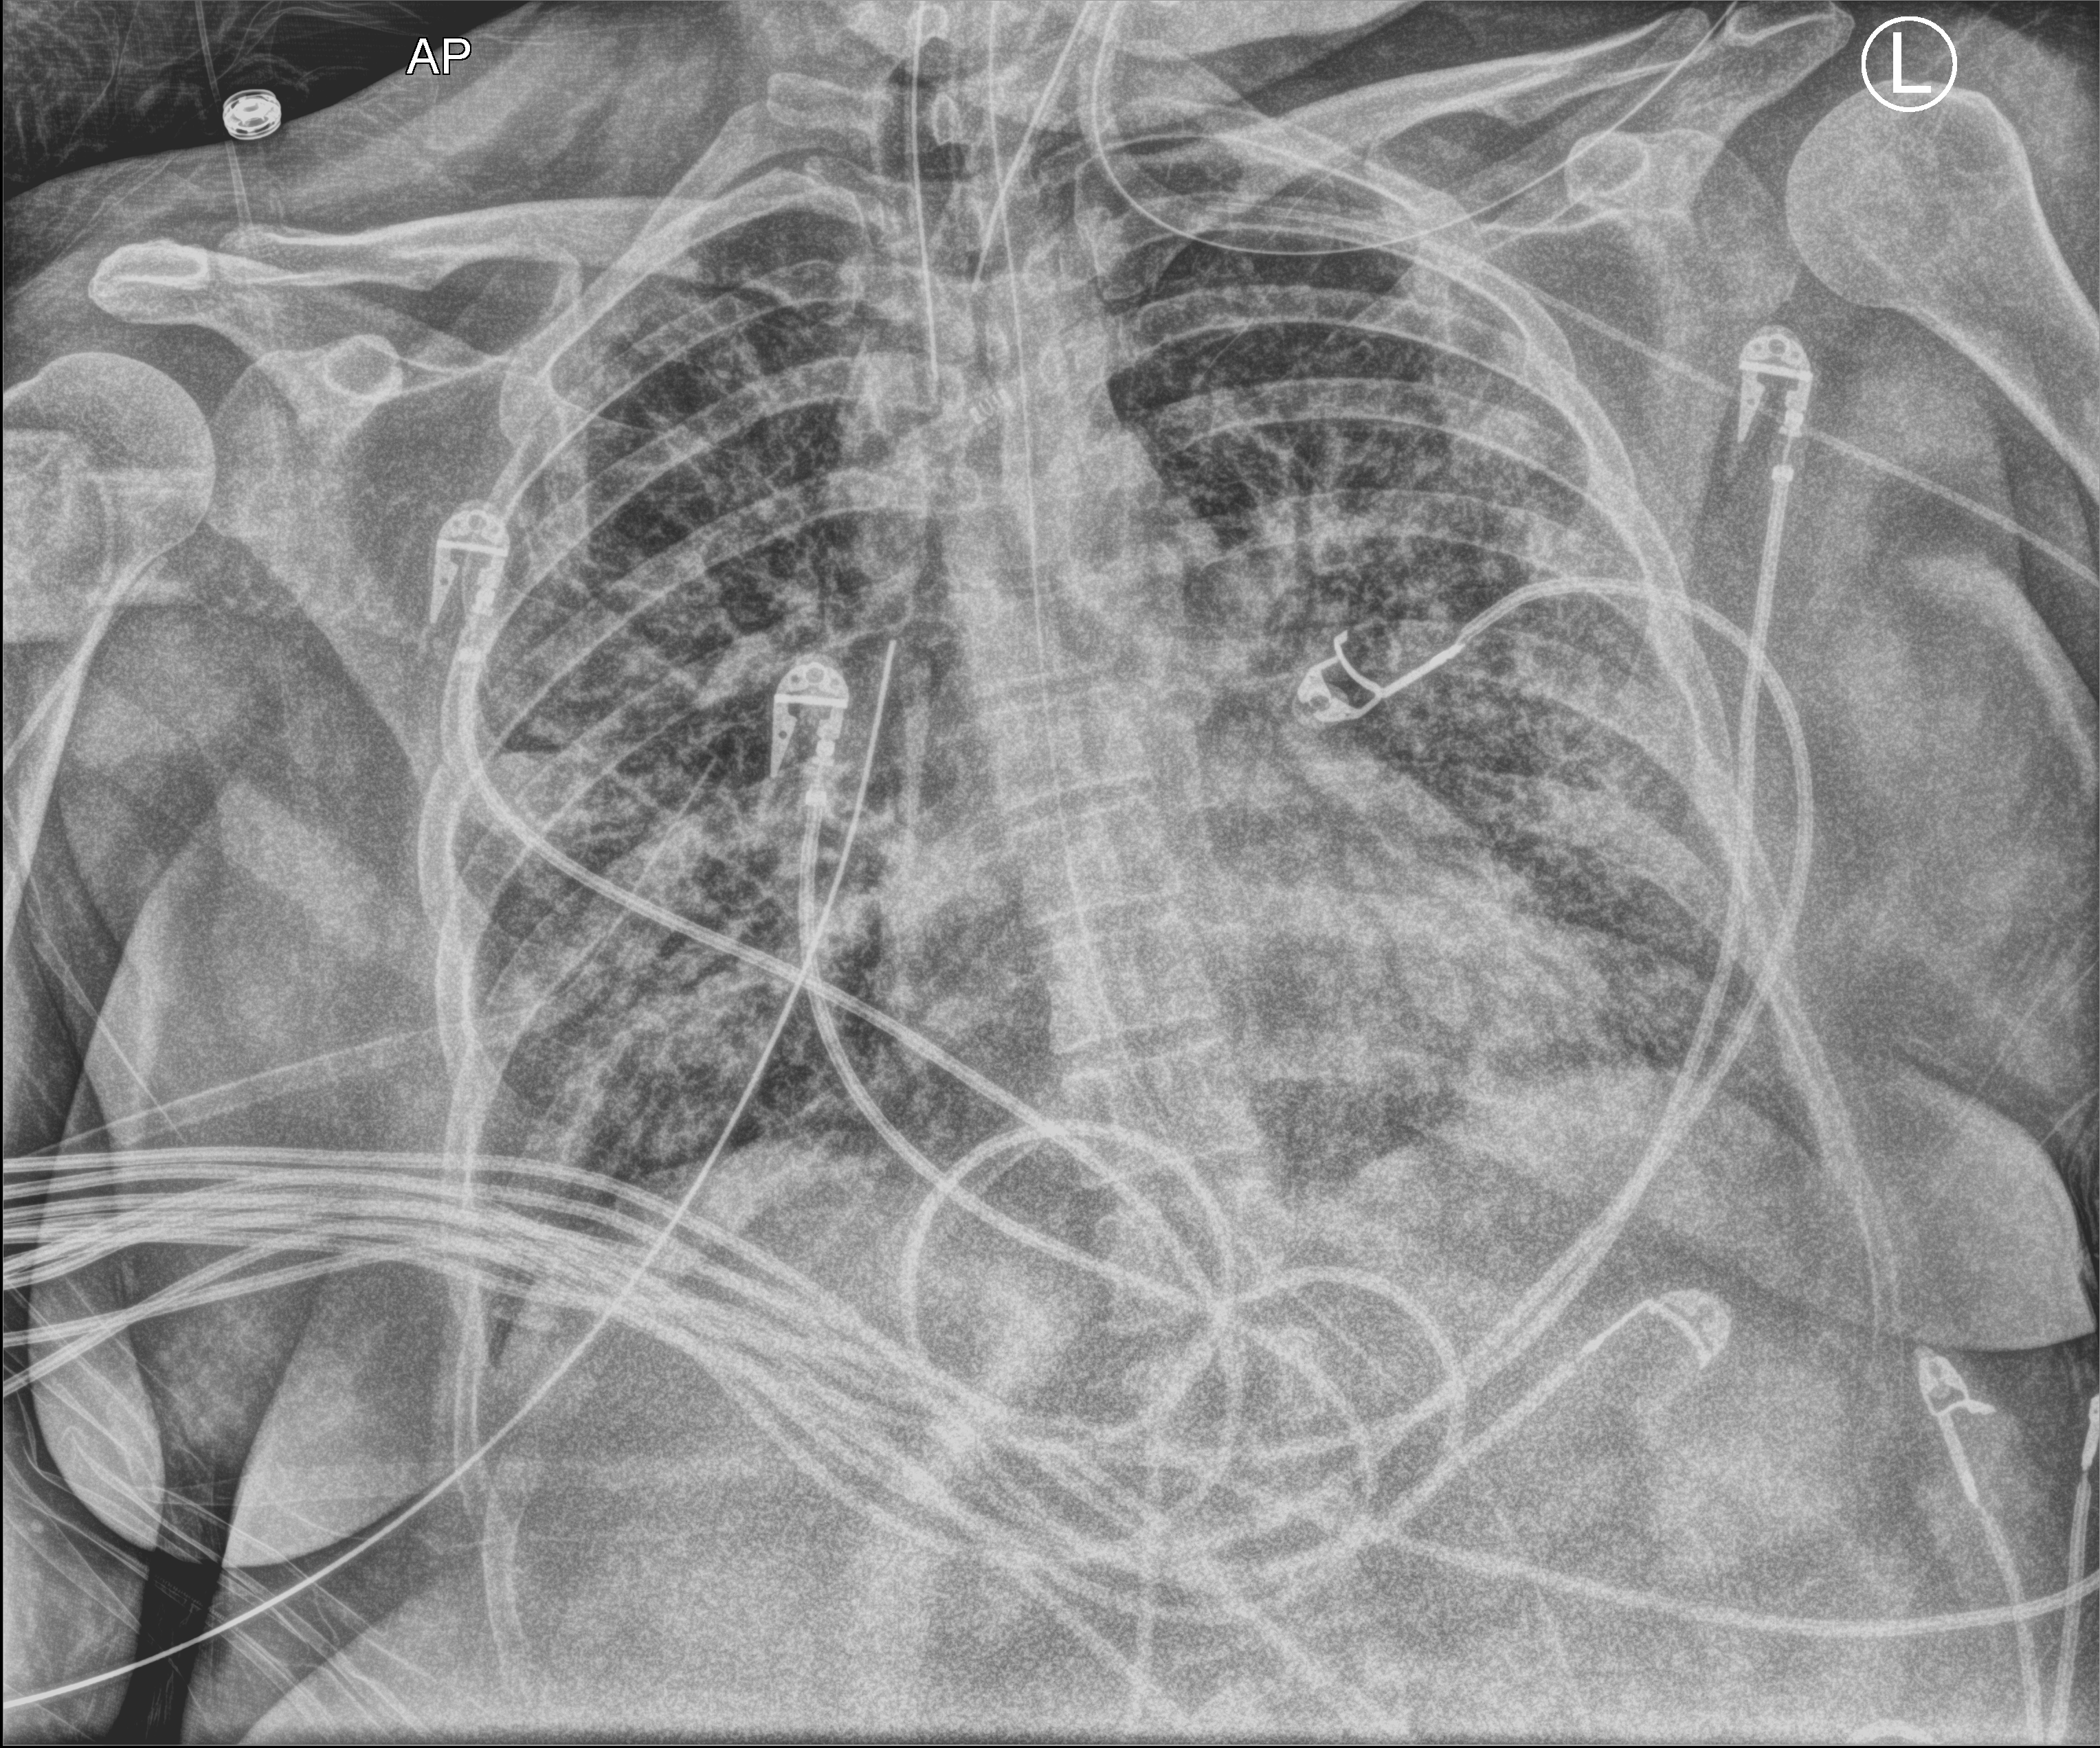
Portable chest radiograph. Patient hospitalised with COVID-19; female, aged 18–59 years.
From the hospital-stay record, not from the radiograph (when in the stay this image was taken is not recorded): admitted to intensive care during this hospital stay: yes.